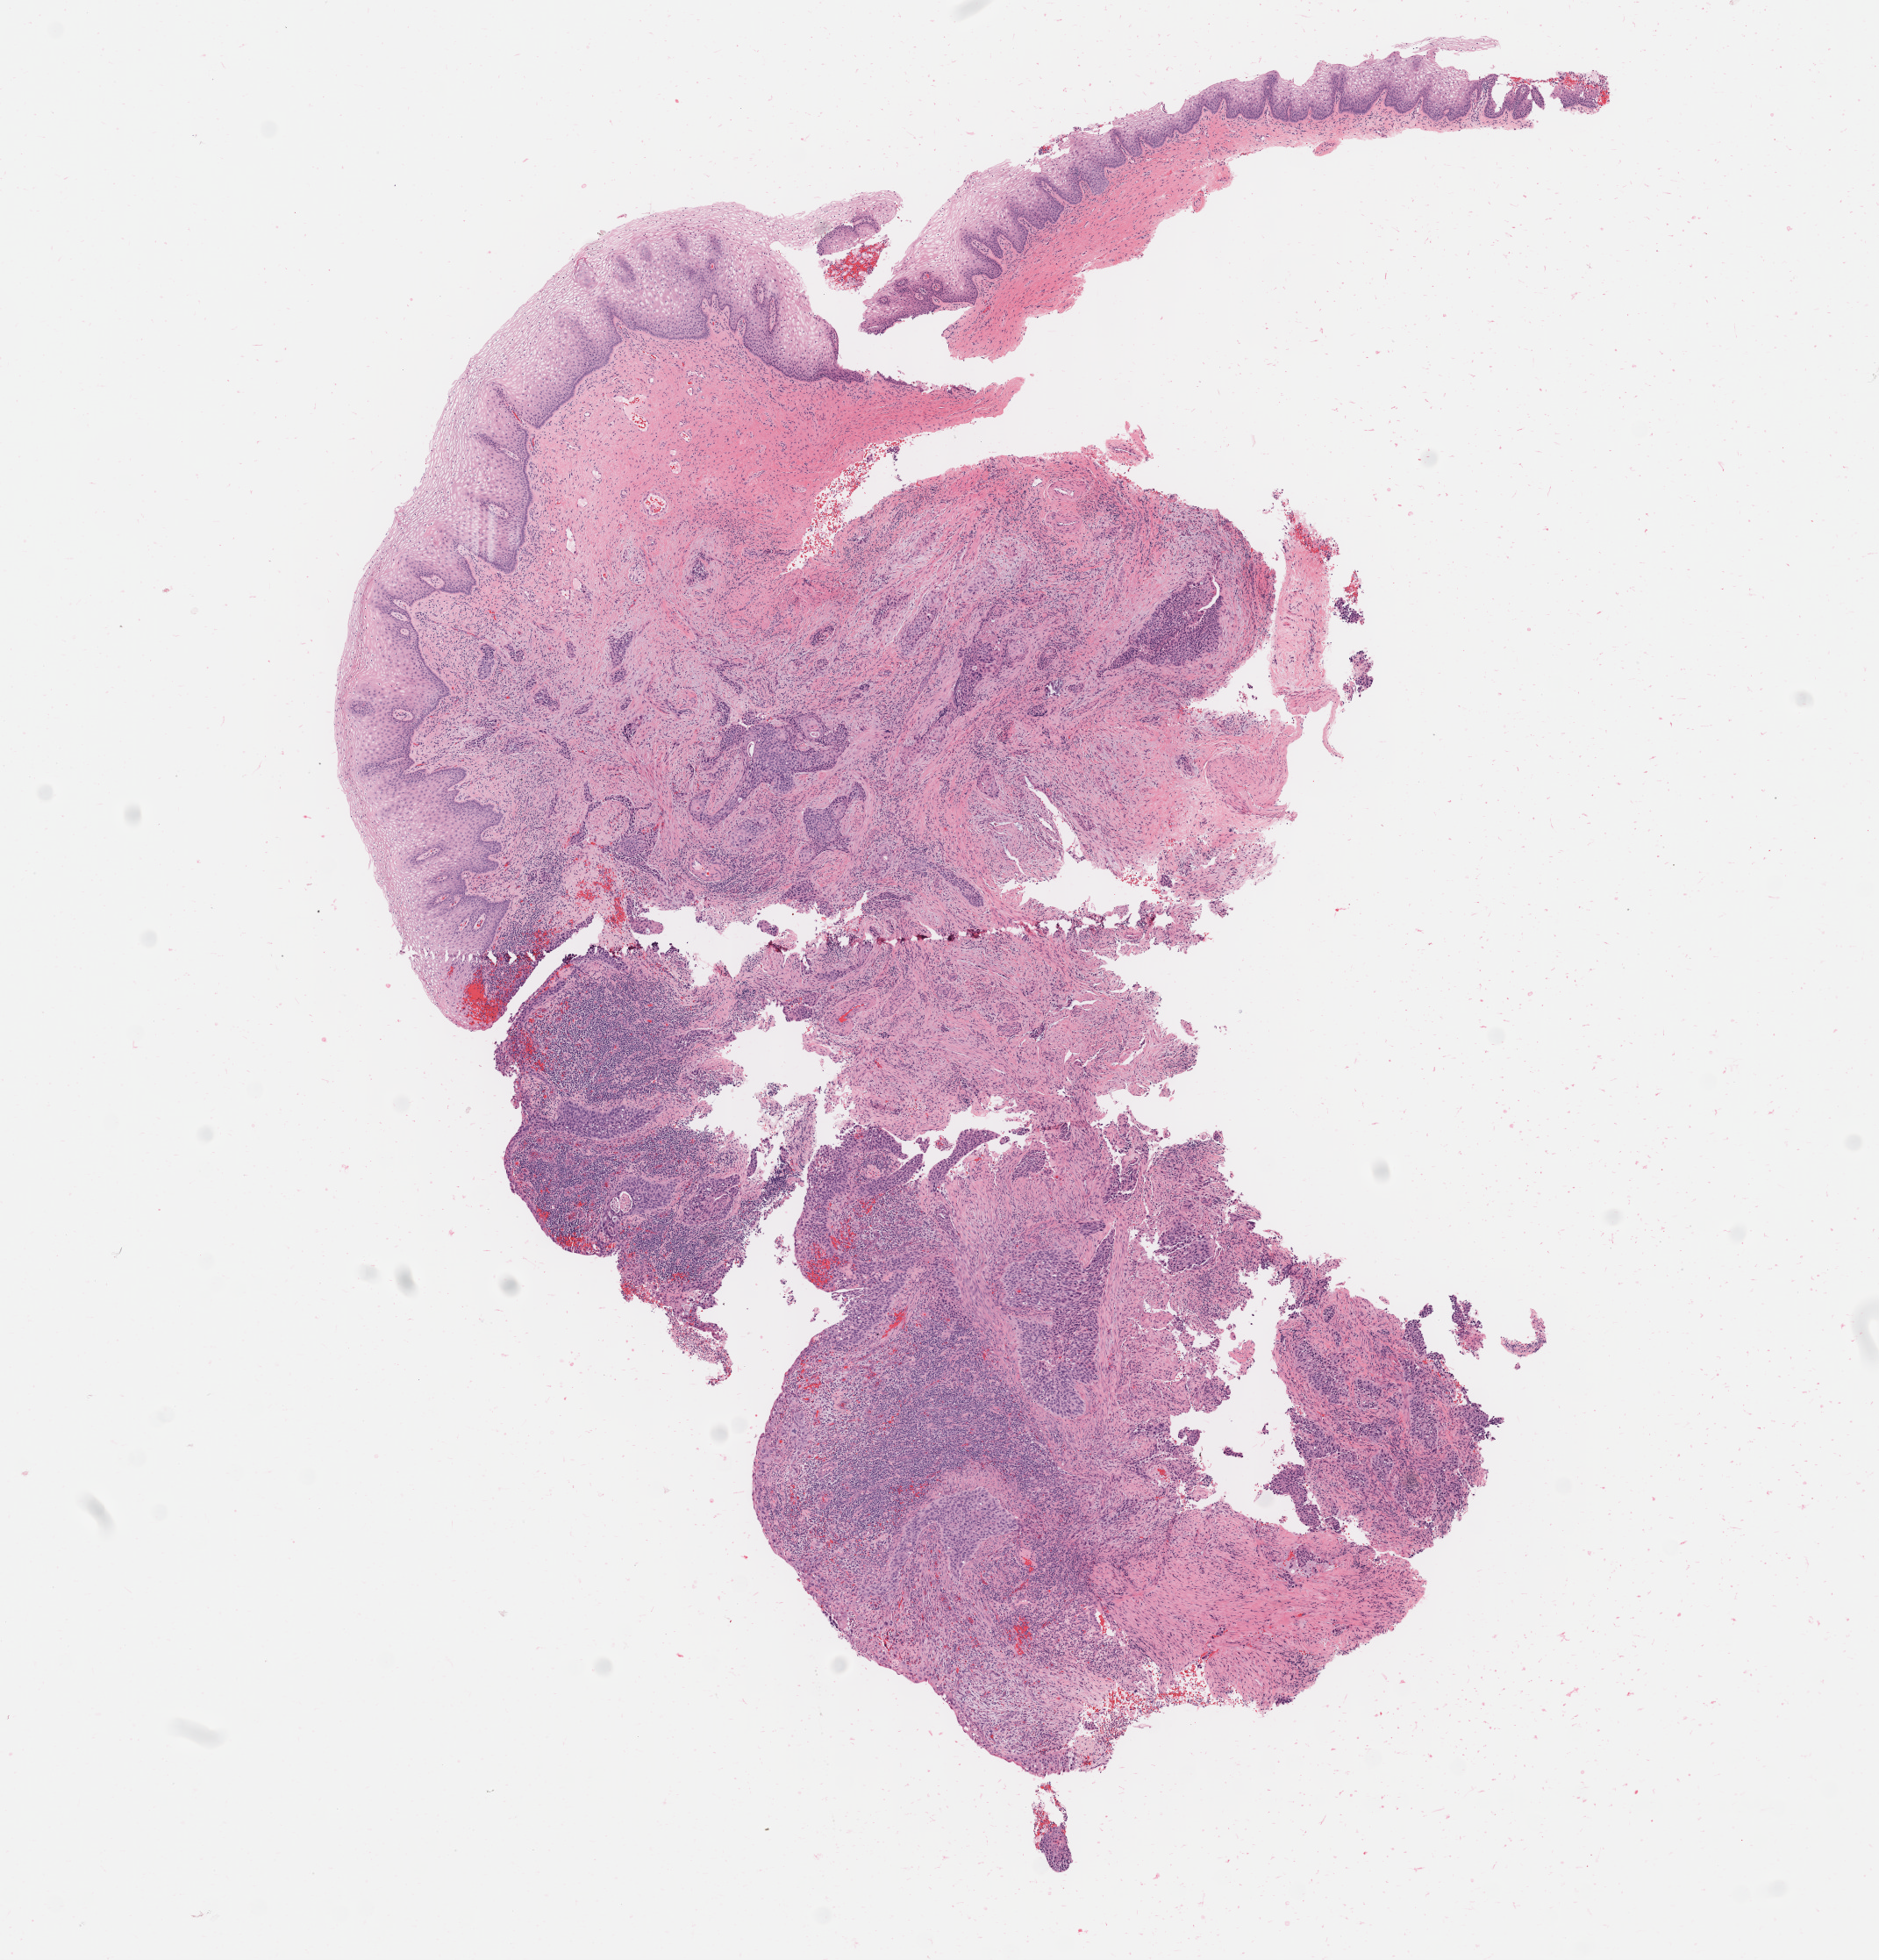
Hematoxylin and eosin (H&E) whole-slide image, whole scanned area (about 8.5 x 8.9 mm) shown as a low-resolution overview. Tumor tissue. Anatomic site: cervix. Patient: female, 39 years old.
* diagnosis: Squamous cell carcinoma, large cell, nonkeratinizing, NOS